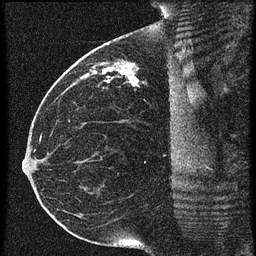
Breast MRI (dynamic contrast-enhanced), one sagittal slice; slice 29 of 60 in the series (ordered by position); 3 images stored at this slice position (order not interpretable as contrast timing); 1.5 T; TE 4.2 ms, TR 20.4 ms; 1.5 mm slice thickness; 256 × 256 image matrix, field of view 200 × 200 mm. Female patient, age 35 years. From the clinical record (not read from this slice): setting: breast cancer imaged before/during neoadjuvant chemotherapy; receptor status: HR-positive, HER2-negative.
Annotated regions visible in this slice (semi-automatically segmented with operator editing):
- analysis volume of interest (the breast-tissue region the enhancement analysis was run in; not a lesion): bounding box (x1, y1, x2, y2) in pixels: (84, 50, 179, 97)
- tumour enhancement mask (voxels above the 90 % enhancement threshold inside the analysis volume of interest): (94, 64, 139, 85)